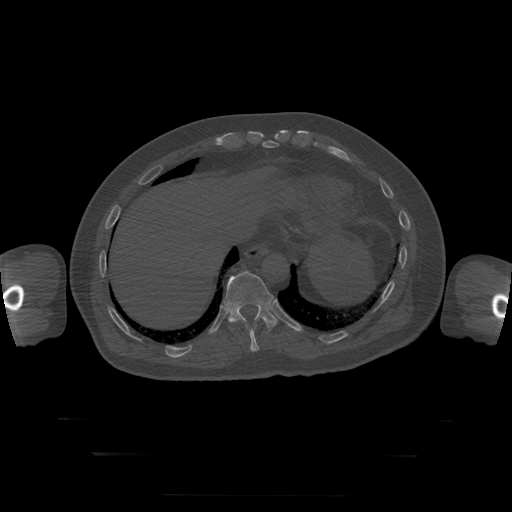
CT including the spine, one axial slice; reconstruction kernel STANDARD; bone window (W 1800 / L 400 HU); 1.25 mm slice thickness; 512 × 512 image matrix, field of view 510 × 510 mm. Patient age 73 years. Case-level facts recorded for this patient, not image findings: primary cancer: prostate.
Outlined on this slice (semi-automatic segmentation, software-assisted and operator-edited):
- T10 vertebra: box from (x=234, y=322) to (x=260, y=352) px
- T11 vertebra: (x=224, y=271)–(x=278, y=330)